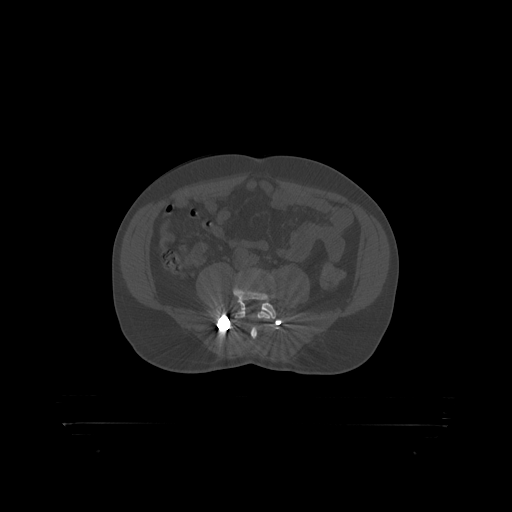
CT including the spine, one axial slice. Slice 219 of 399 in the series (ordered by position). Bone window (W 1800 / L 400 HU). 1.25 mm slice thickness. 512 × 512 image matrix, field of view 650 × 650 mm. Male patient, age 46 years. Case-level facts recorded for this patient, not image findings: primary cancer: skin.
Structures marked on this image (semi-automatic segmentation, software-assisted and operator-edited):
- L4 vertebra: bounding box (x1, y1, x2, y2) in pixels: (235, 311, 272, 319)
- L5 vertebra: (234, 287, 277, 319)